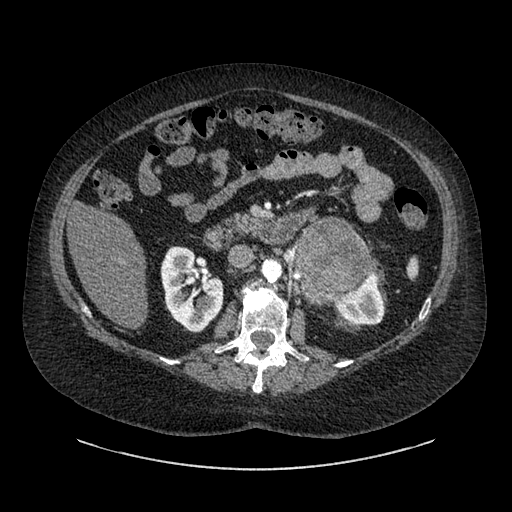
Contrast-enhanced abdominal CT, one axial slice; slice 518 of 769 in the series (ordered by position); reconstruction kernel SOFT; 120 kVp; intravenous contrast given; soft-tissue window (W 400 / L 40 HU); 0.62 mm slice thickness; 512 × 512 image matrix, field of view 460 × 460 mm. Female patient, age 61 years. Case-level facts recorded for this patient, not image findings: diagnosis: adrenocortical carcinoma; tumour side: left adrenal; tumour size at pathology: 13 cm.
Outlined on this slice (semi-automatically segmented with operator editing):
- mass: bounding box (x1, y1, x2, y2) in pixels: (298, 220, 368, 300)